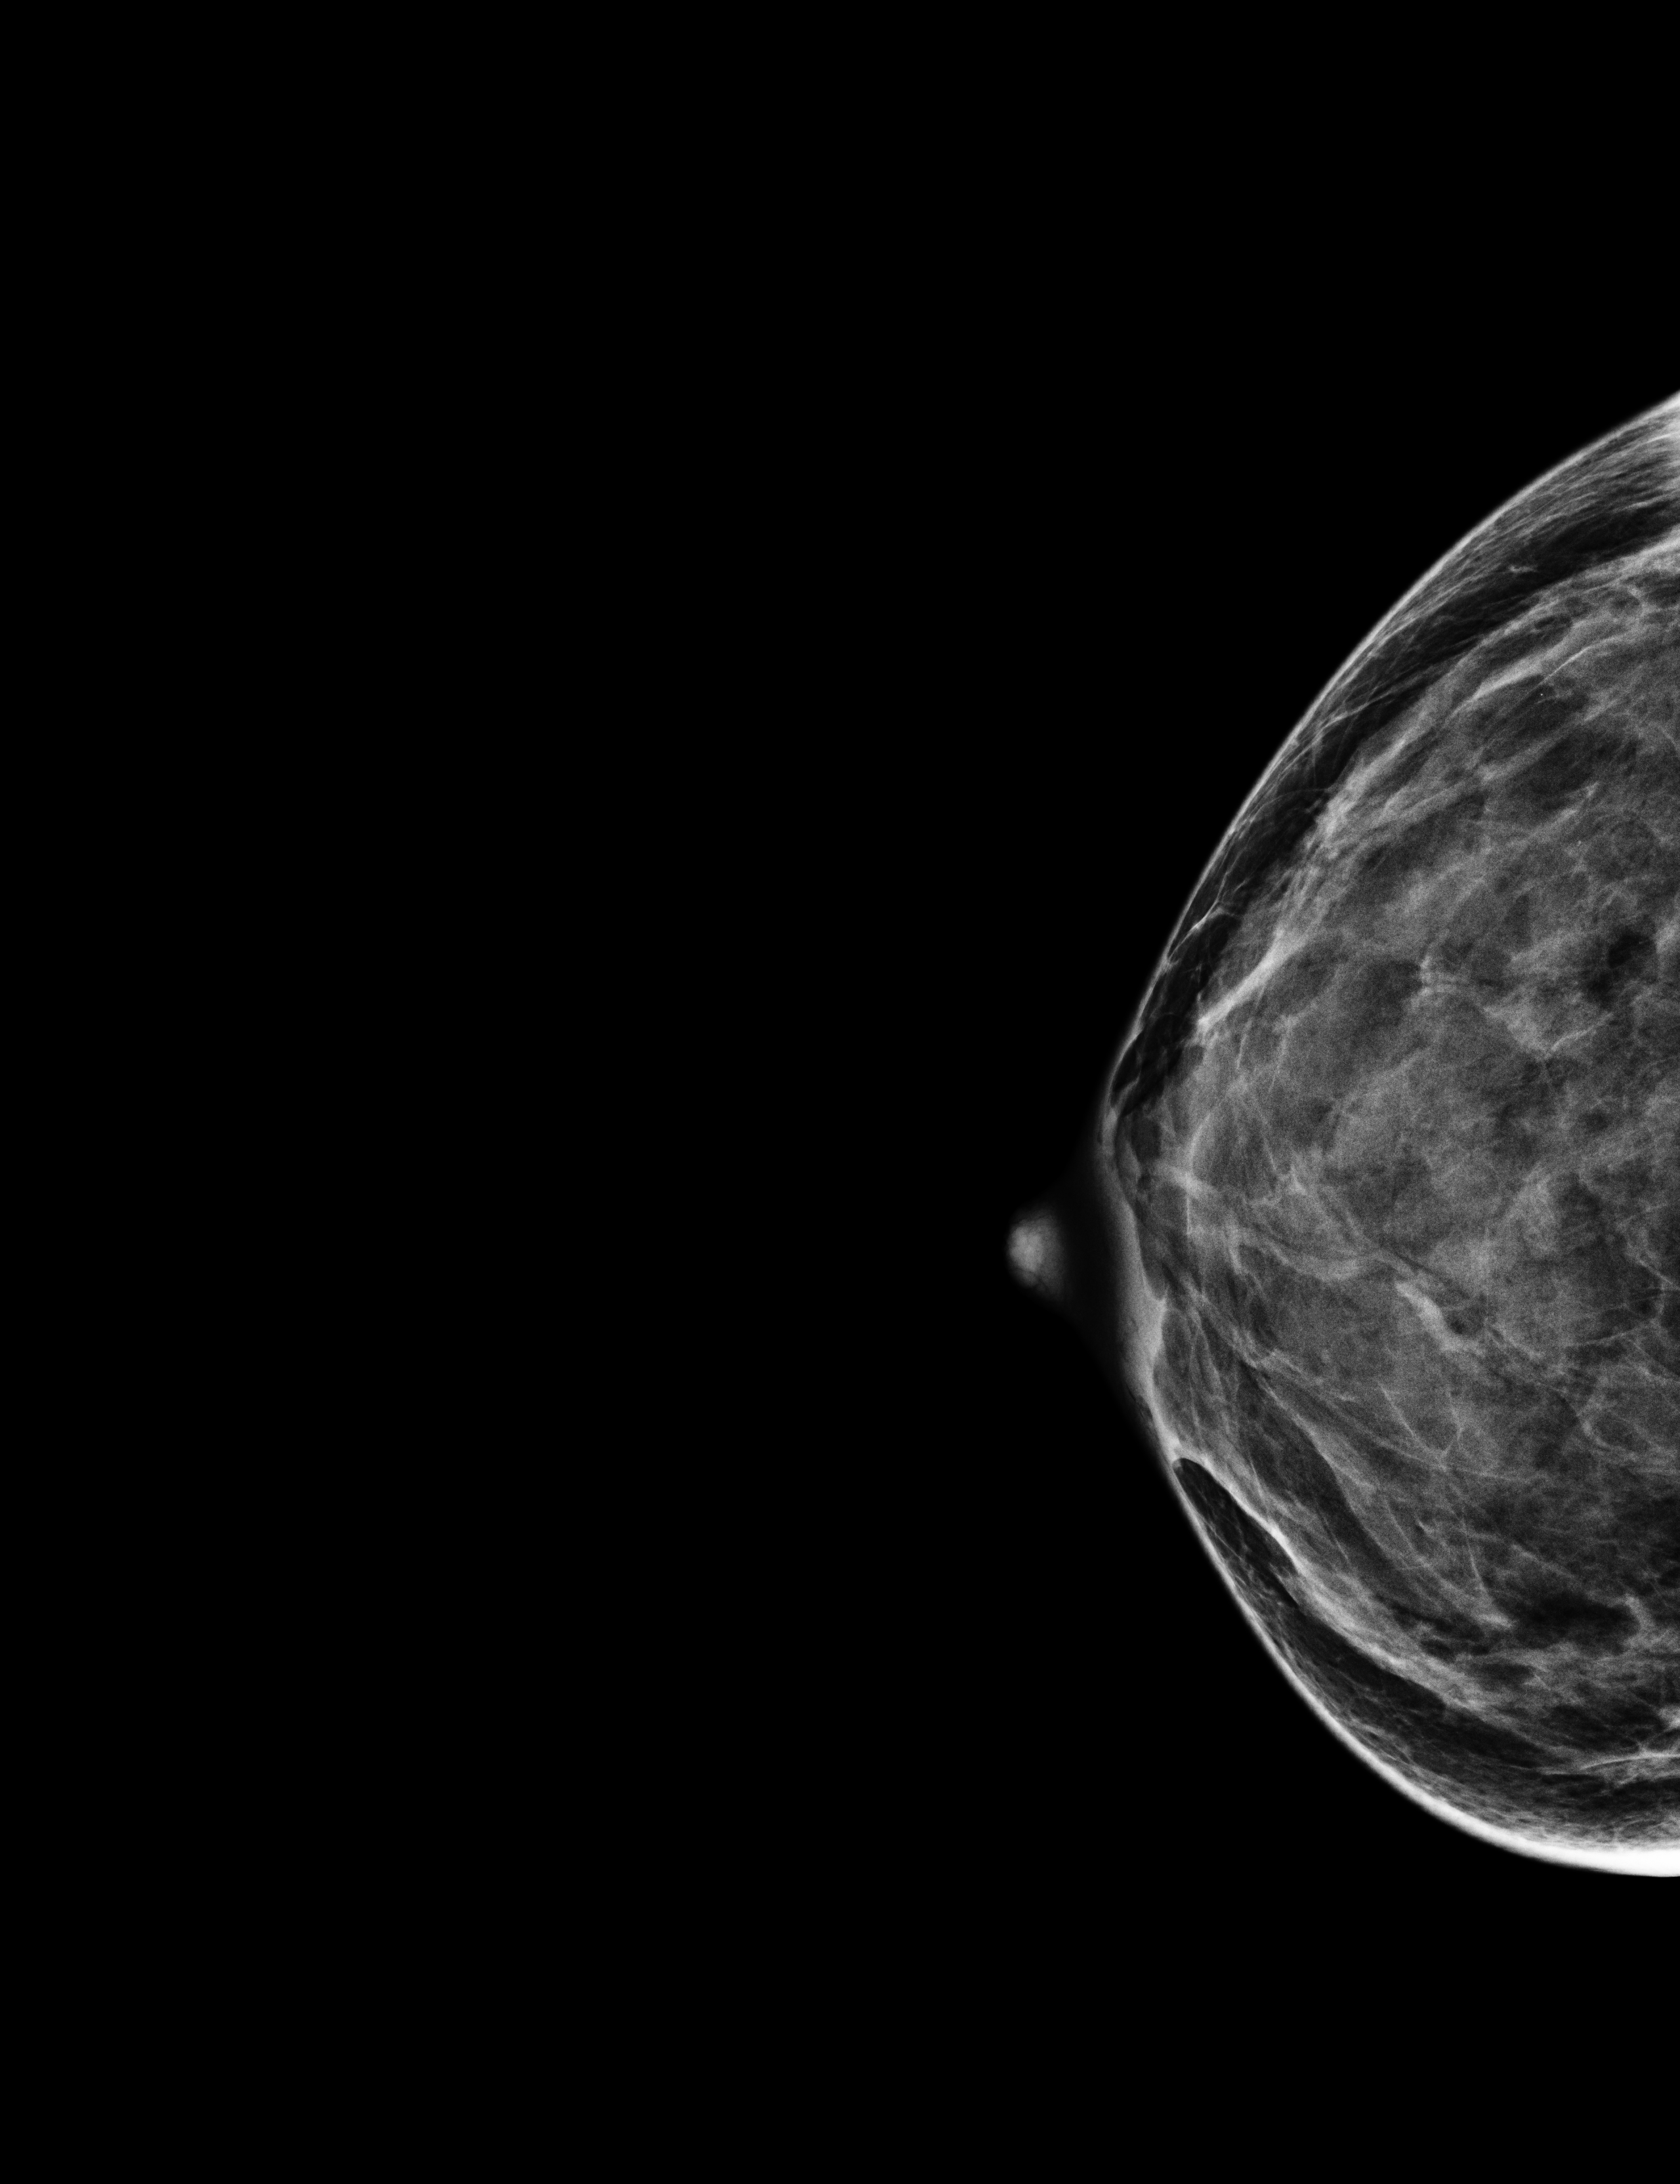
Annual screening mammography examination. Patient aged 43 years (female).
Image type: full-field digital mammogram. Breast: right. Projection: CC view.